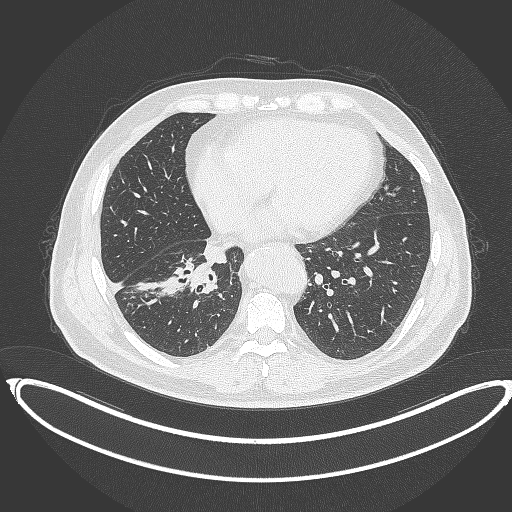
Chest CT, one axial slice. Reconstruction kernel B70f. Lung window (W 1500 / L -600 HU). 1 mm slice thickness. 512 × 512 image matrix, field of view 448 × 448 mm. Male patient, age 61 years. Case-level facts recorded for this patient, not image findings: clinical TNM (as recorded): T1b N1 M0.
Outlined on this slice (bounding box drawn by a radiologist):
- lung tumour (recorded histology: squamous cell carcinoma): box from (x=162, y=259) to (x=217, y=300) px